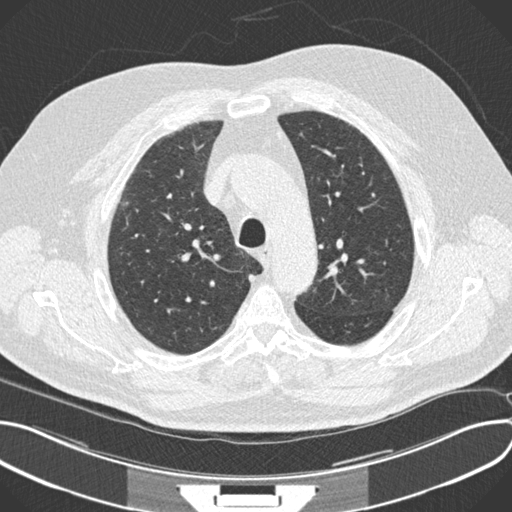
Low-dose screening chest CT, axial slice. Third annual screen. Lung window (W 1500 / L -600 HU). Standard (soft-tissue) reconstruction kernel (B30f). 120 kVp. 512 × 512 image matrix, field of view 380 × 380 mm. Male participant, aged 64 years at enrolment. Current smoker at enrolment.
- Expert reader's lesion annotation, bounding box (x1, y1, x2, y2) in pixels: (109, 185, 141, 221).
- Screening reader's record for this exam (one nodule recorded; not confirmed to be the boxed lesion): non-calcified nodule or mass ≥4 mm, right upper lobe, 7 × 6 mm, smooth margins, soft tissue attenuation, pre-existing on the prior screen: no.
- Official screen result: positive, other.